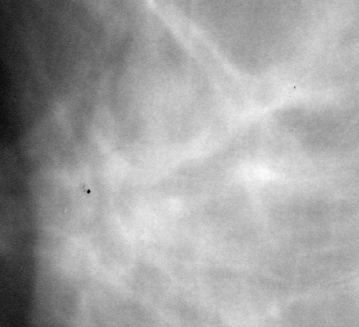
Cropped region of a digitized screen-film mammogram centred on a radiologist-marked abnormality, right breast, MLO view.
- Mass, shape lobulated, margins ill defined; BI-RADS assessment category 5; pathology (as recorded): malignant.